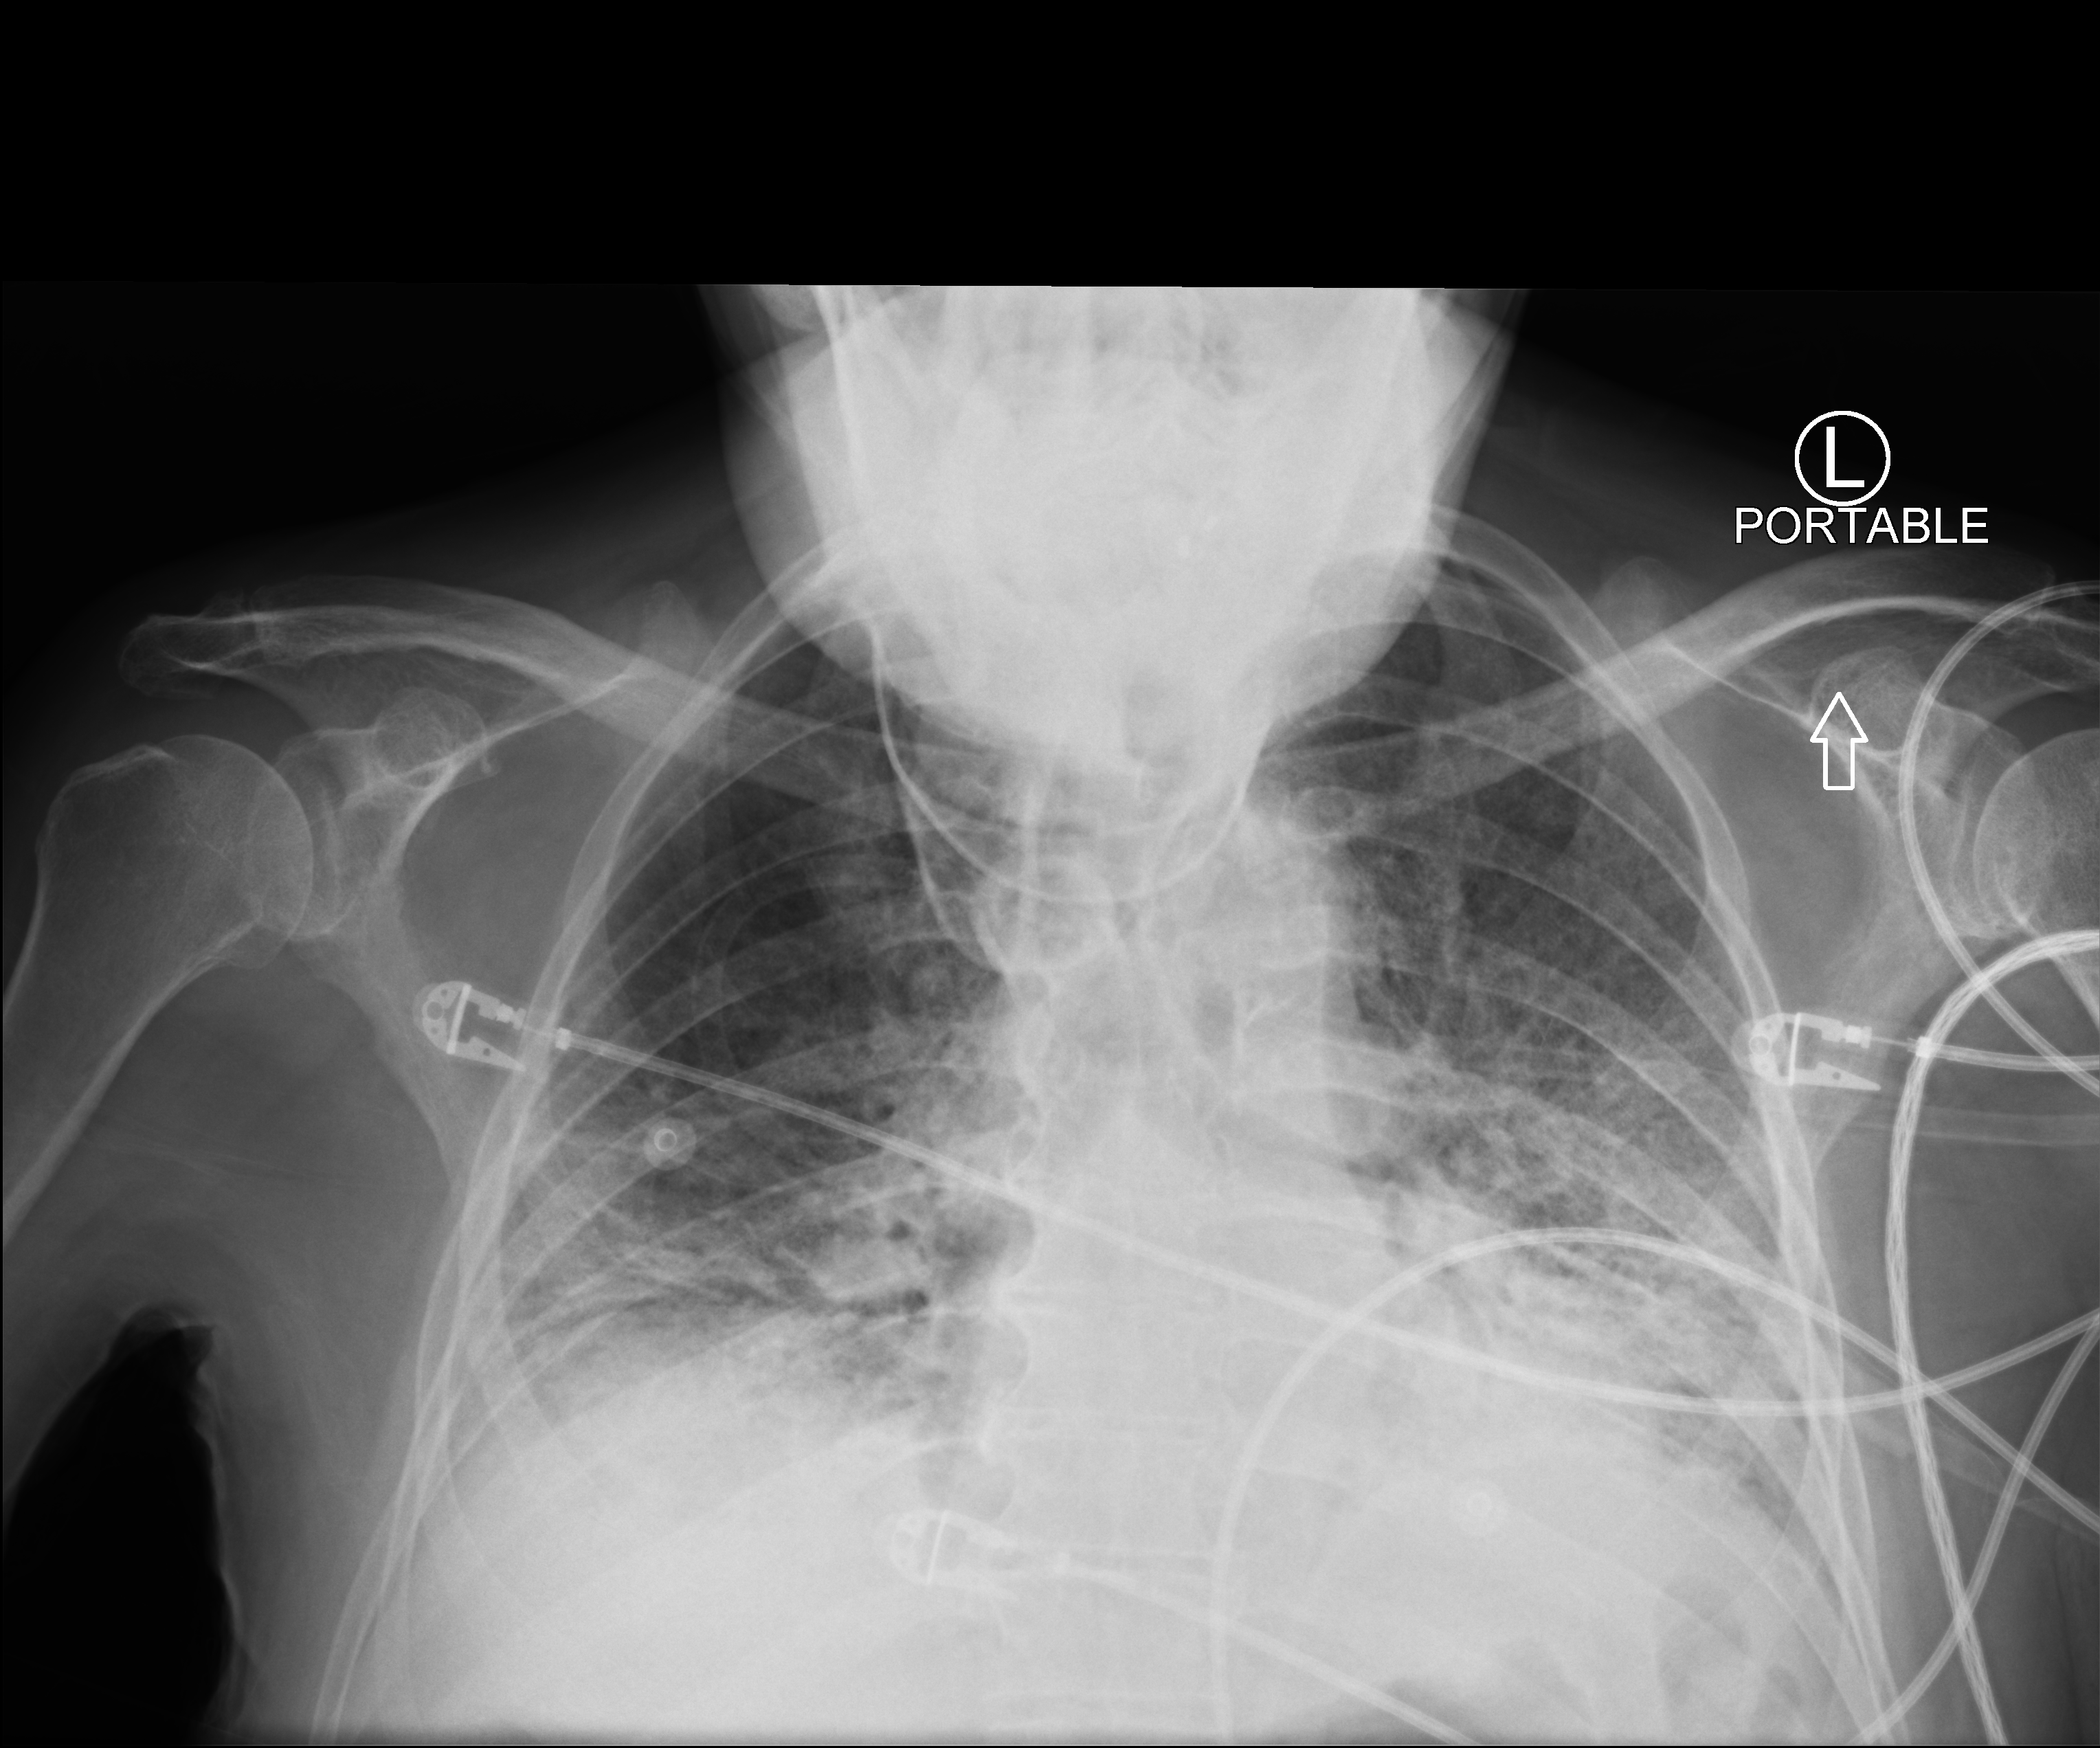
Portable chest radiograph; anteroposterior (AP) projection. Patient hospitalised with COVID-19; male, aged 75–90 years.
Admission-level facts for this patient (not findings on this image; timing relative to this image not recorded): COPD (admission record): no.